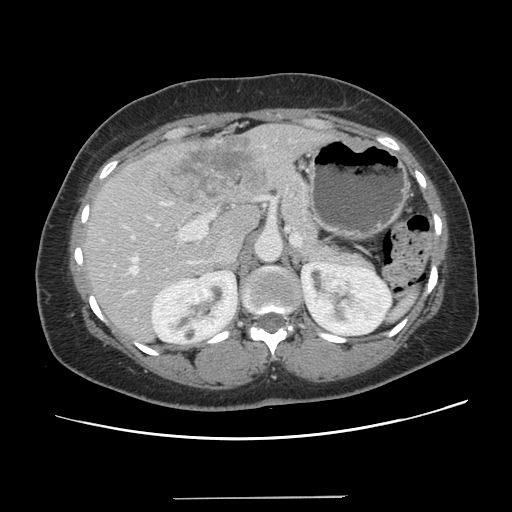
Contrast-enhanced abdominal CT, one axial slice; position 78 of 141 along the scan axis; 120 kVp; intravenous contrast given; soft-tissue window (W 400 / L 40 HU); 2.5 mm slice thickness; 512 × 512 image matrix, field of view 366 × 366 mm. Female patient, age 53 years. Case-level facts recorded for this patient, not image findings: diagnosis: colorectal cancer liver metastases, imaged before liver resection; multiple liver metastases: no; largest metastasis: 14.5 cm; disease in both lobes: yes.
Annotated regions visible in this slice (manually delineated by an expert):
- hepatic veins: bounding box <128,257,137,274> (left, top, right, bottom; pixels)
- liver: <85,125,328,342>
- planned liver remnant (the part of the liver to remain after resection): <86,205,260,342>
- portal vein (with intrahepatic branches): <131,201,207,271>
- liver metastasis: <166,136,265,204>